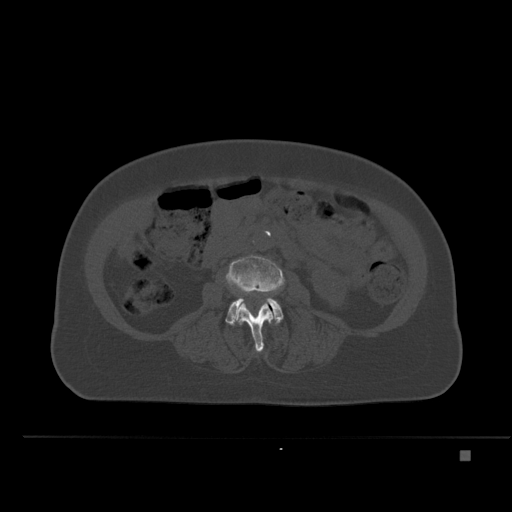
CT including the spine, one axial slice. Bone window (W 1800 / L 400 HU). 512 × 512 image matrix, field of view 422 × 422 mm. Female patient, age 74 years. From the clinical record (not read from this slice): primary cancer: colon.
Structures marked on this image (semi-automatically segmented with operator editing):
- L3 vertebra: bounding box <226,256,285,352> (left, top, right, bottom; pixels)
- L4 vertebra: <225,286,283,326>